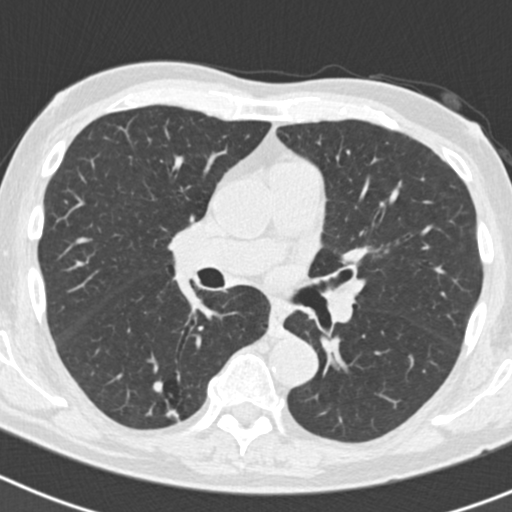
Low-dose screening chest CT, axial slice; second screening round (one year after baseline); lung window (W 1500 / L -600 HU); standard (soft-tissue) reconstruction kernel (B30f); 120 kVp; slice 78 of 186 in the series; 512 × 512 image matrix. Male participant, aged 70 years at enrolment. Current smoker at enrolment.
- Expert reader's lesion annotation, box from (x=132, y=374) to (x=199, y=433) px.
- The screening reader recorded 5 non-calcified nodules or masses ≥4 mm on this exam; which of them this box marks is not recorded.
- Later outcome: lung cancer diagnosed 622 days after this screen — bronchiolo-alveolar adenocarcinoma, NOS, right lower lobe, poorly differentiated (G3), stage IB (AJCC 6th edition), 30 mm at pathology.